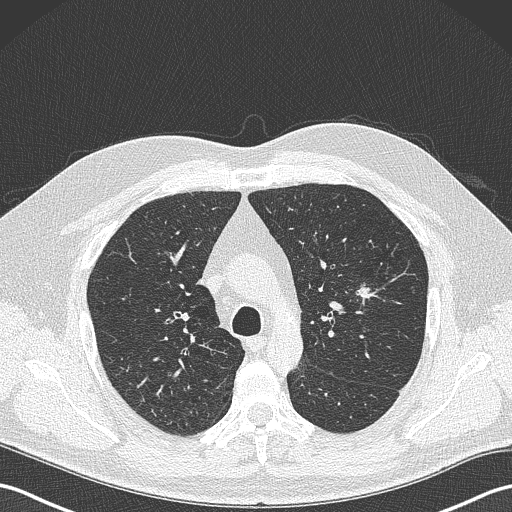
Low-dose screening chest CT, one axial slice. Slice 241 of 343 in the series (ordered by position). Reconstruction kernel B50f. 120 kVp. Lung window (W 1500 / L -600 HU). 1 mm slice thickness. 512 × 512 image matrix, field of view 350 × 350 mm.
Structures marked on this image (manually delineated by an expert):
- lesion 1 (tumor, upper lobe of left lung): bounding box (x1, y1, x2, y2) in pixels: (357, 285, 374, 302)